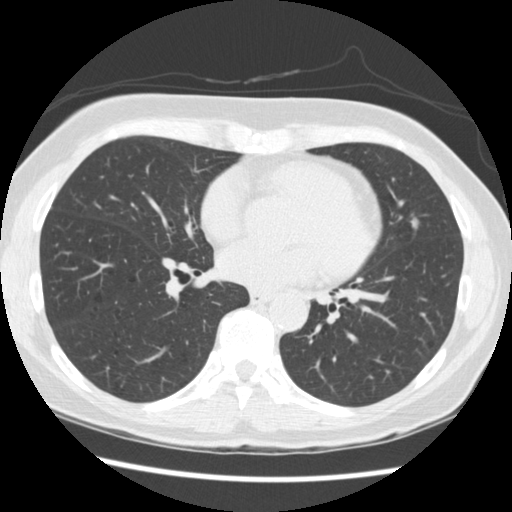
Low-dose screening chest CT, axial slice. Third screening round (two years after baseline). Lung window (W 1500 / L -600 HU). 2.5 mm slice thickness. Standard (soft-tissue) reconstruction kernel (STANDARD). 120 kVp. Slice 139 of 262 in the series. Female participant, aged 60 years at enrolment.
- Lesion marked by an expert reader, box from (x=392, y=206) to (x=434, y=249) px.
- Screening reader's record for this exam (one nodule recorded; not confirmed to be the boxed lesion): non-calcified nodule or mass ≥4 mm, lingula, 6 × 5 mm, smooth margins, soft tissue attenuation, pre-existing on the prior screen: yes; interval growth: yes.
- Official screen result: positive, other.